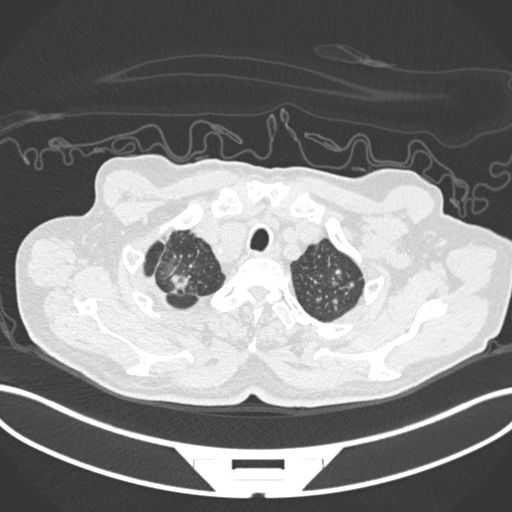
Chest CT, one axial slice. Position 200 of 207 along the scan axis. Reconstruction kernel B30f. 120 kVp. Lung window (W 1500 / L -600 HU). 1 mm slice thickness. 512 × 512 image matrix, field of view 400 × 400 mm. Patient: male, 69 years. Case-level facts recorded for this patient, not image findings: clinical TNM (as recorded): T1c N1 M1.
Outlined on this slice (rectangle marked by the reading radiologist):
- lung tumour (recorded histology: adenocarcinoma): box from (x=165, y=266) to (x=195, y=296) px